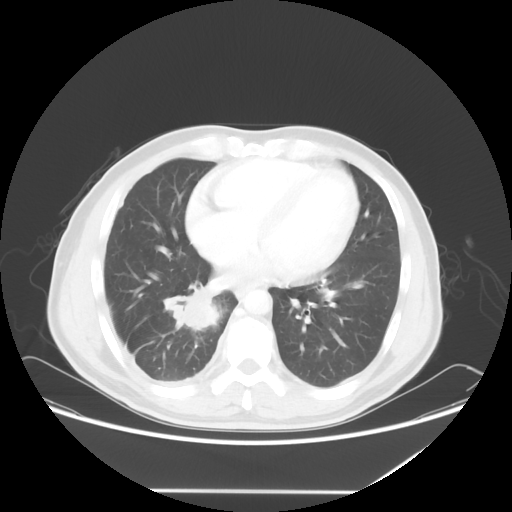
Chest CT, one axial slice; slice 23 of 60 in the series (ordered by position); reconstruction kernel STANDARD; 120 kVp; lung window (W 1500 / L -600 HU); 5 mm slice thickness; 512 × 512 image matrix, field of view 419 × 419 mm. Male patient, age 48 years. Case-level facts recorded for this patient, not image findings: clinical TNM (as recorded): T3 N3 M1a.
Annotated regions visible in this slice (bounding box drawn by a radiologist):
- lung tumour (recorded histology: squamous cell carcinoma): bounding box <162,281,228,336> (left, top, right, bottom; pixels)